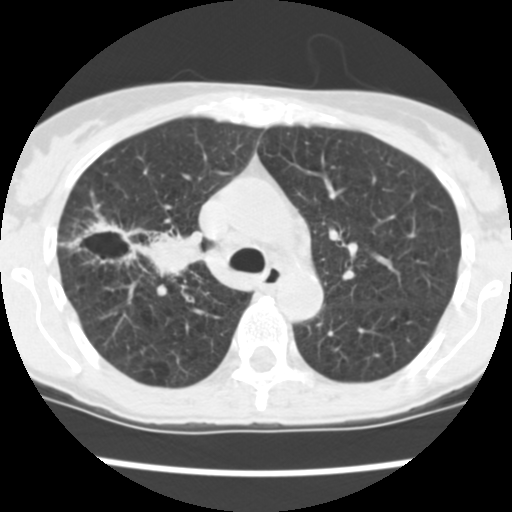
Low-dose screening chest CT, one axial slice; slice 168 of 252 in the series (ordered by position); reconstruction kernel STANDARD; lung window (W 1500 / L -600 HU); 512 × 512 image matrix, field of view 276 × 276 mm.
Structures marked on this image (outlined manually by an expert reader):
- lesion 2 (tumor, lower lobe of right lung): bounding box (x1, y1, x2, y2) in pixels: (65, 217, 203, 276)